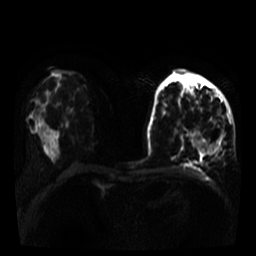
Breast MRI, one axial slice; slice 18 of 35 in the series (ordered by position); diffusion-weighted series; image 2 of 4 stored at this slice position (different b-values; order by instance number); 3 T; 5 mm slice thickness; 256 × 256 image matrix, field of view 320 × 320 mm. Female patient.
Structures marked on this image (outlined manually by an expert reader):
- tumour on diffusion-weighted imaging: bounding box (x1, y1, x2, y2) in pixels: (192, 131, 219, 154)